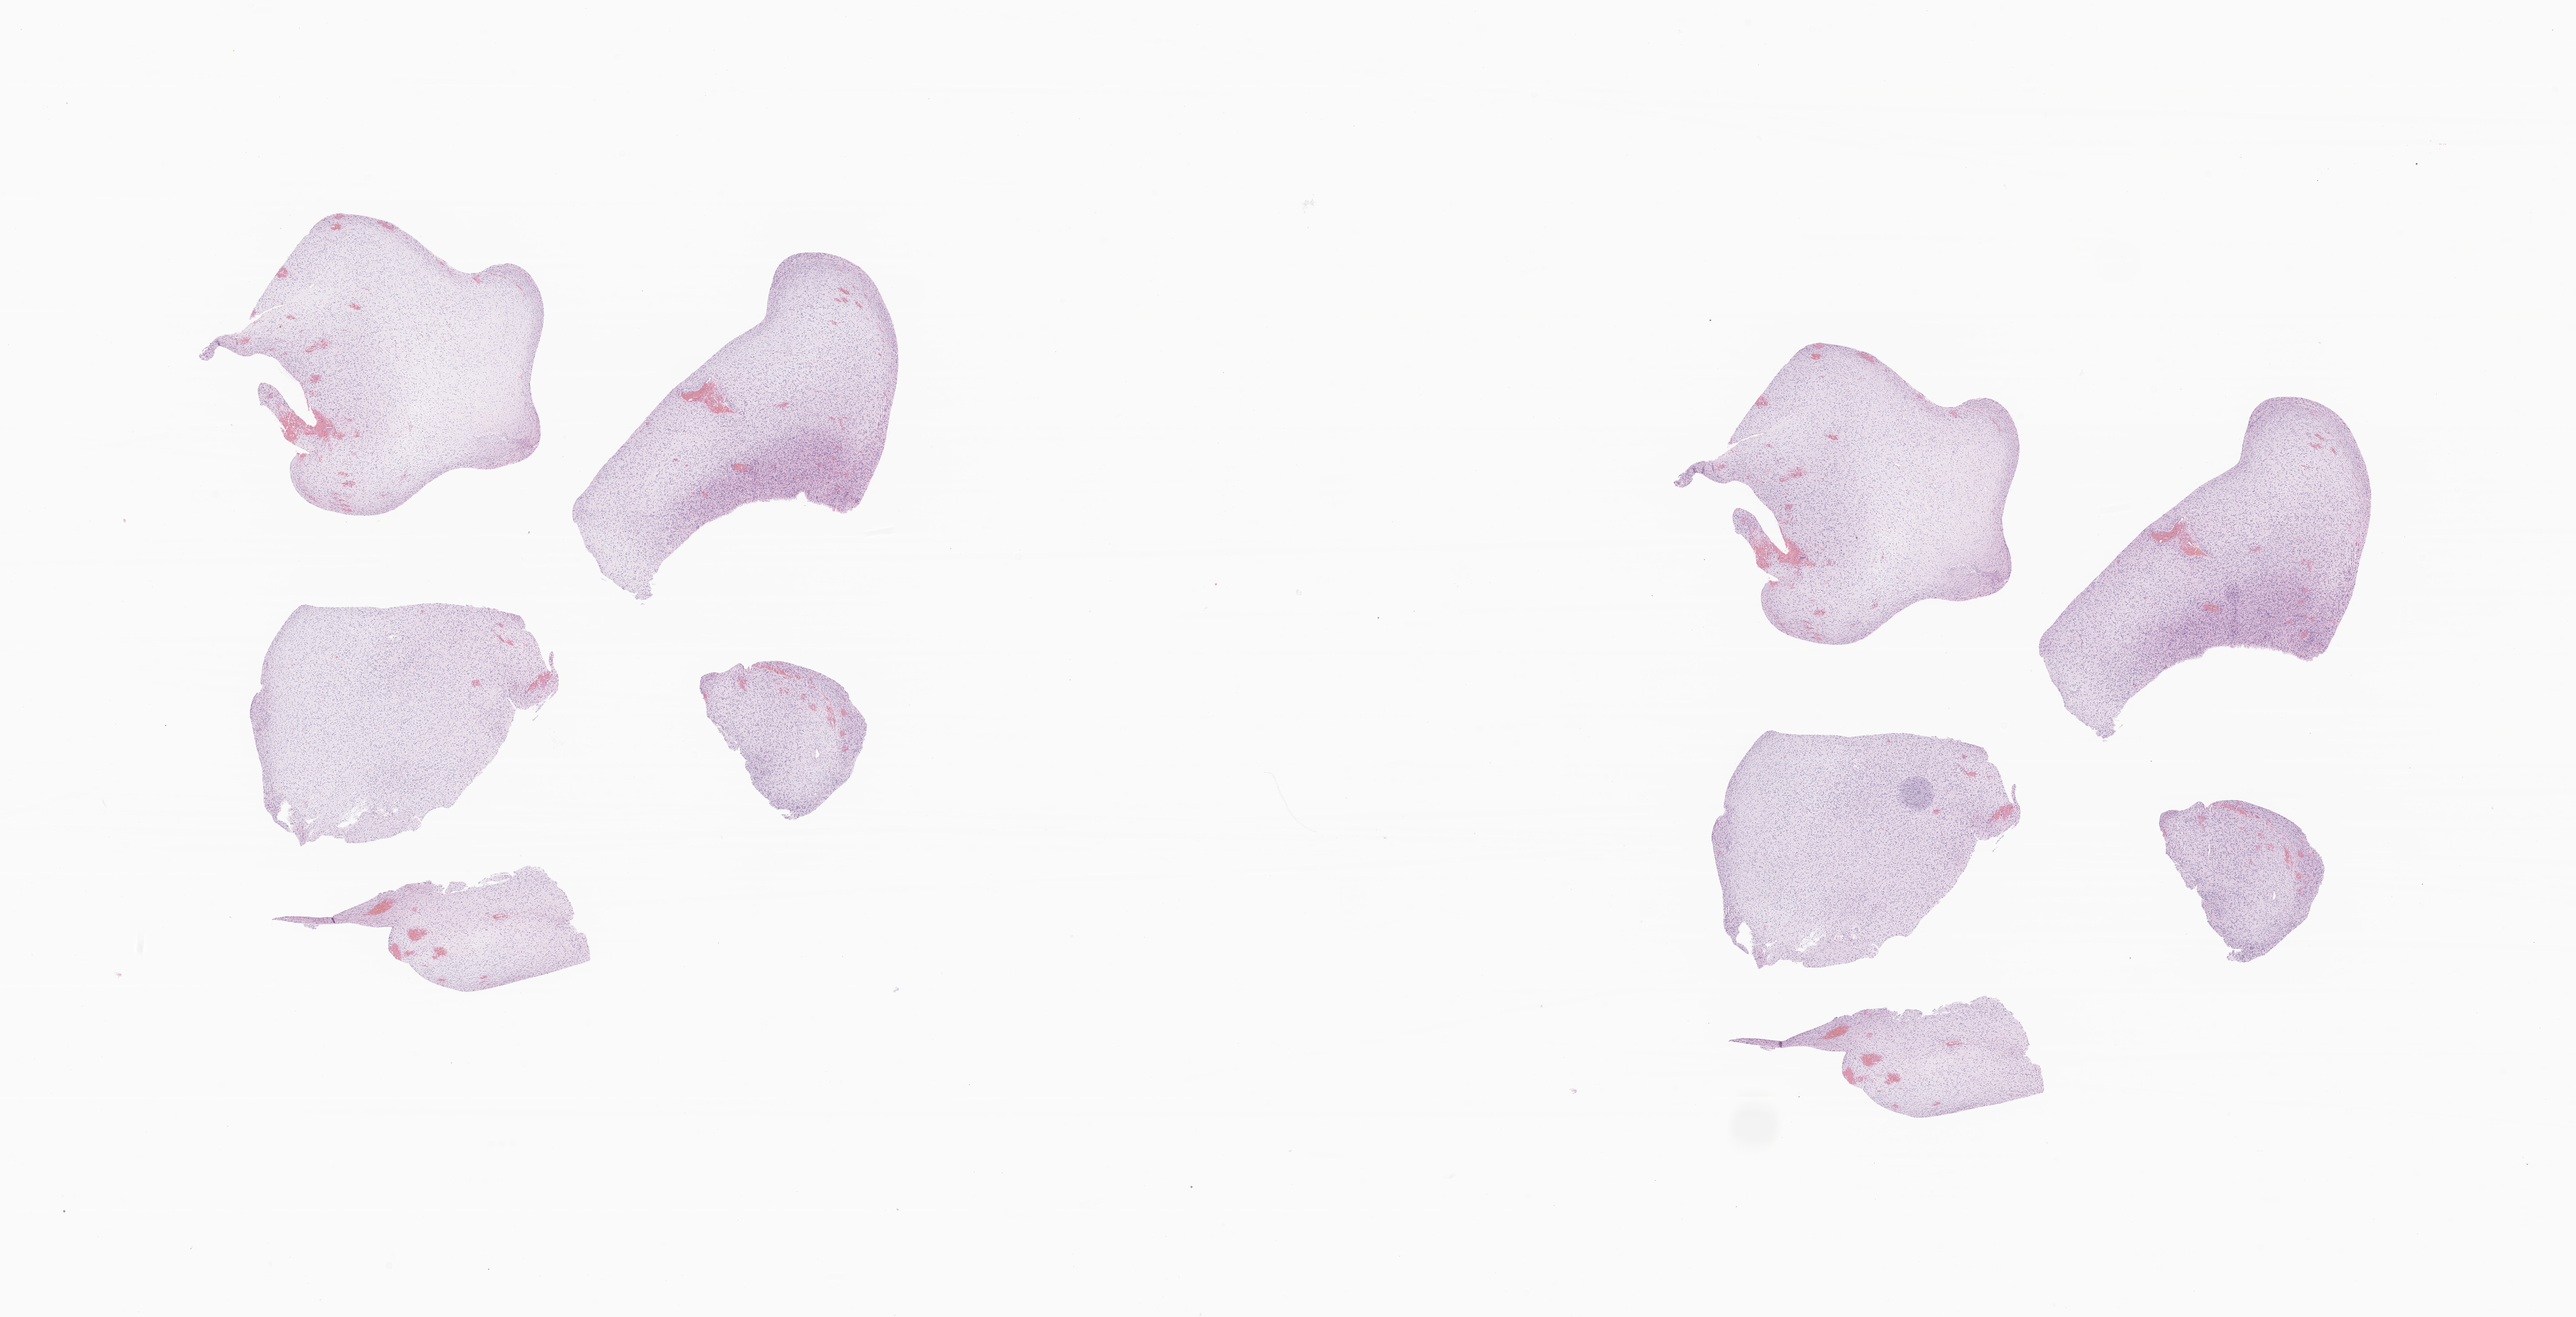
Haematoxylin and eosin whole-slide image of tumor tissue from the brain, a low-resolution overview of the entire scanned area, about 24.5 x 12.5 mm, formalin-fixed paraffin-embedded section. Female patient, age 77 months (6 years 5 months).
• diagnosis: Glioma, malignant